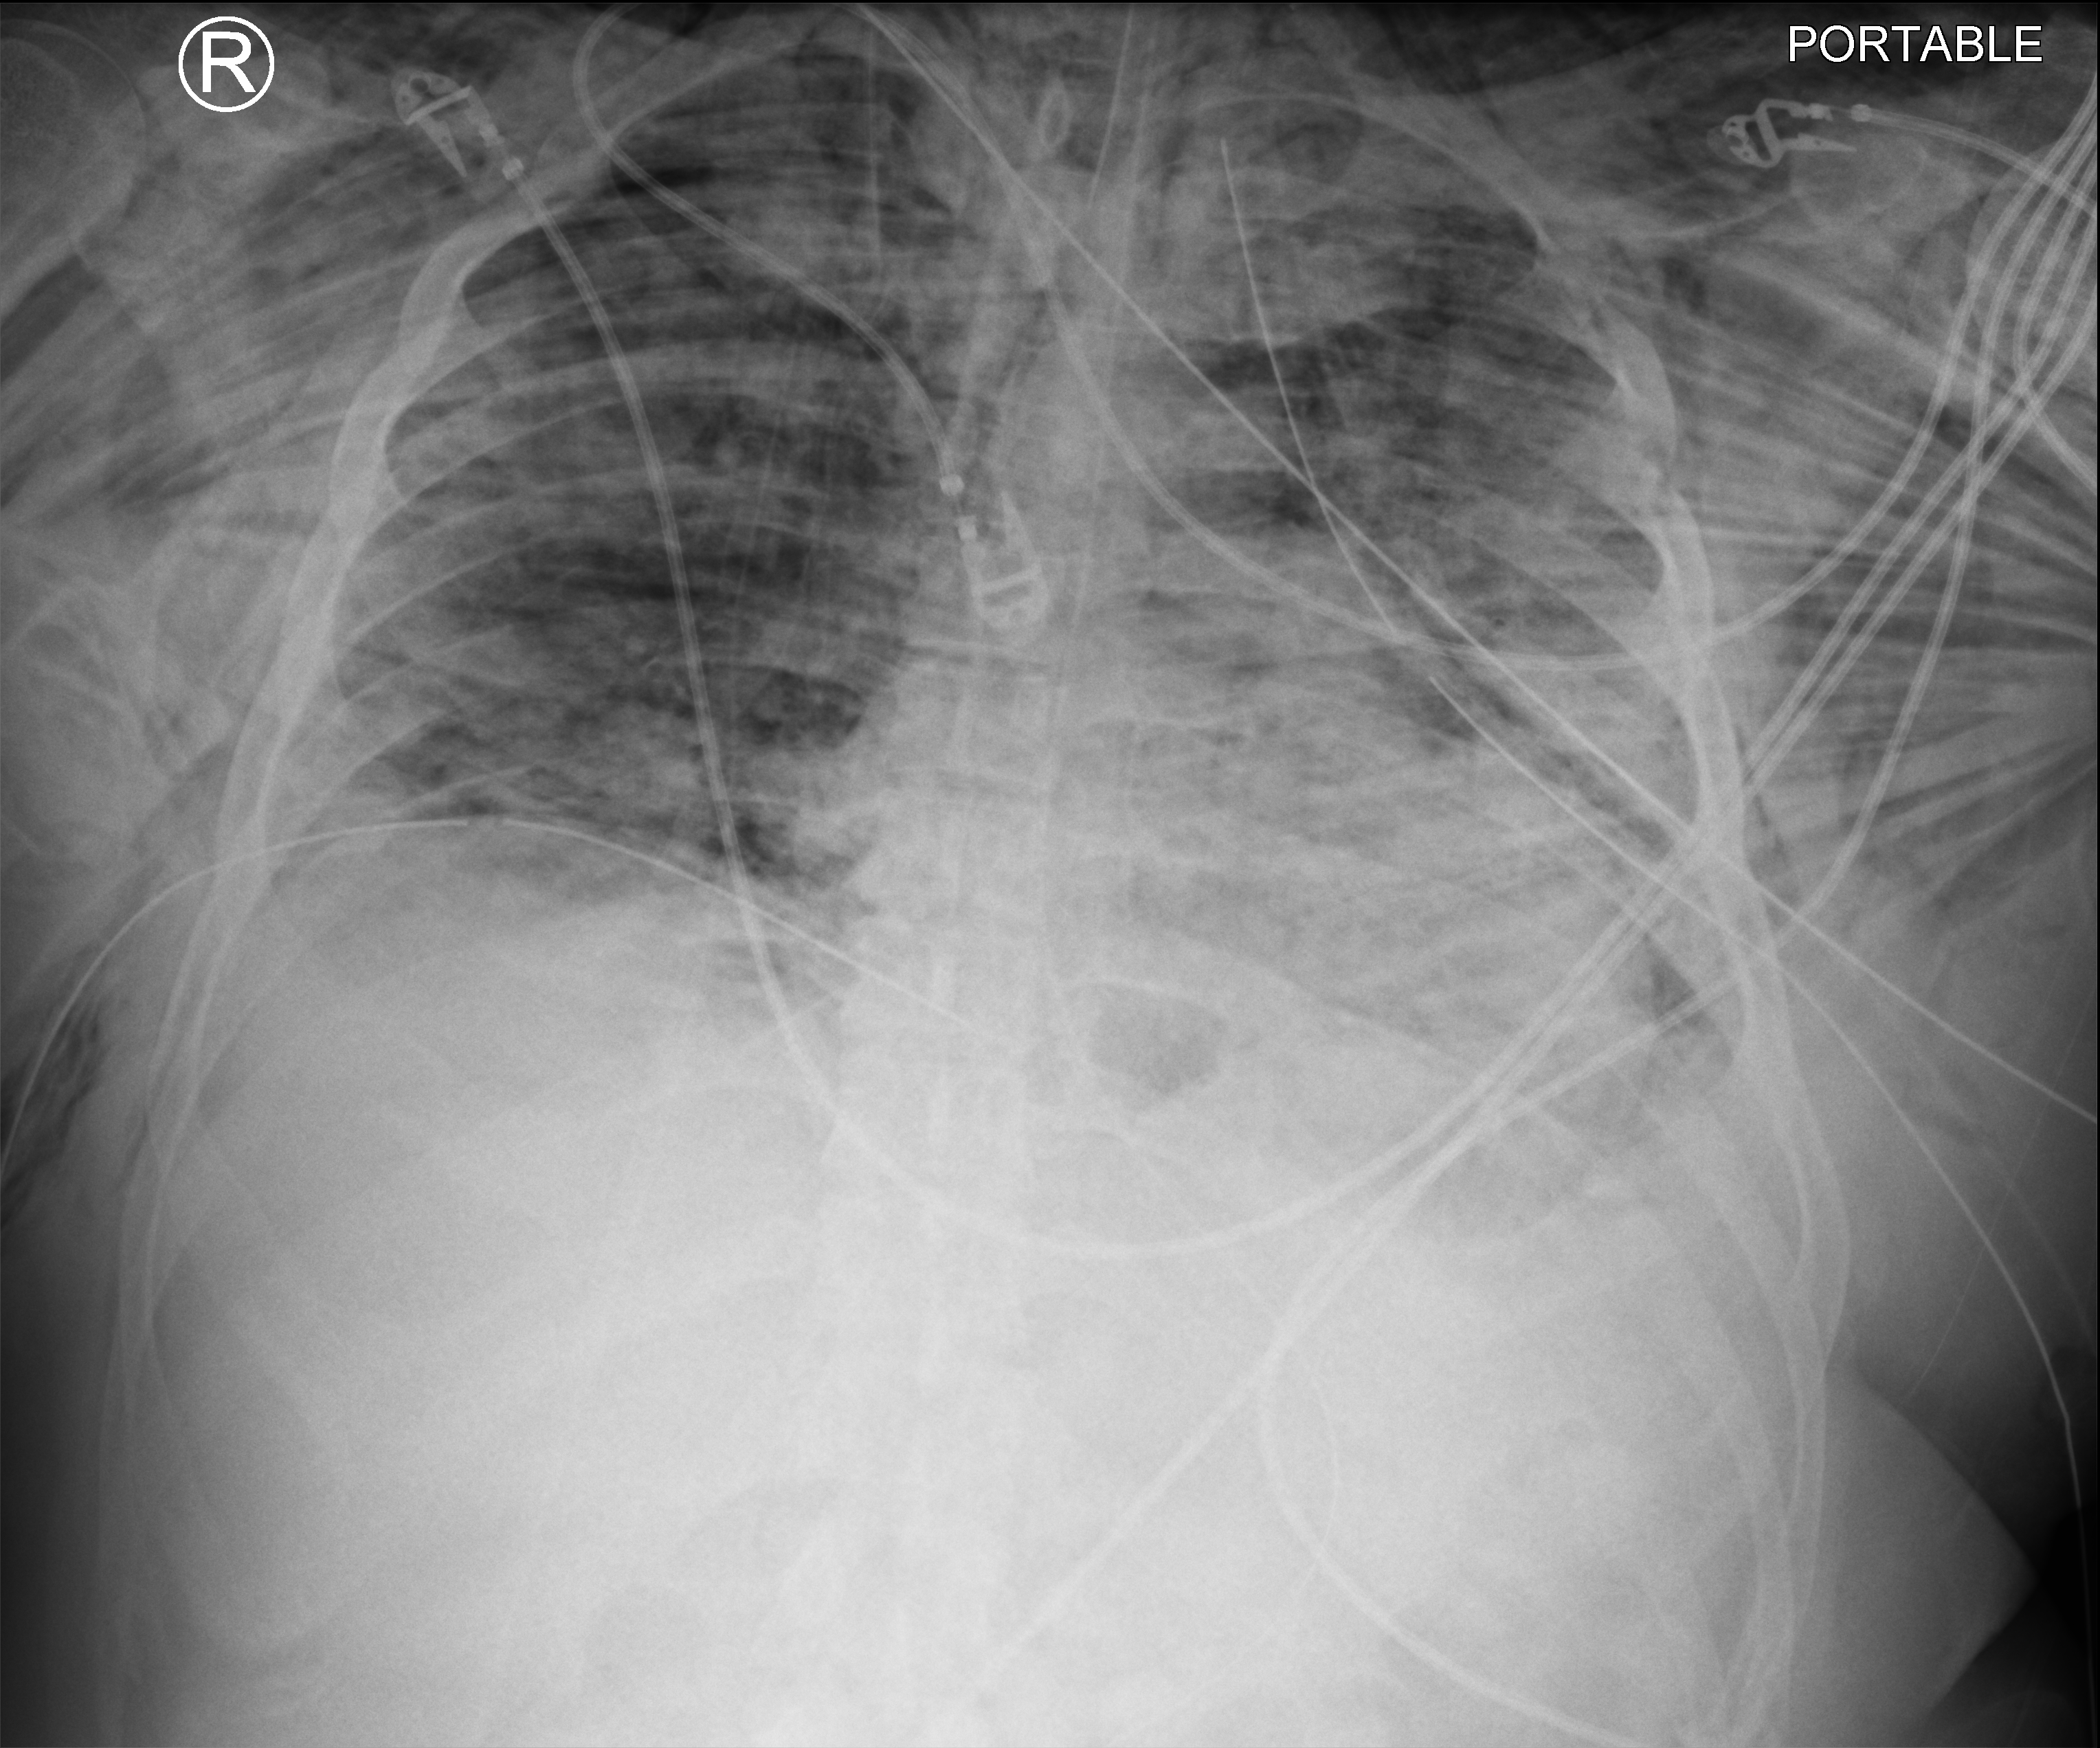
Chest X-ray (portable); anteroposterior (AP) projection. Patient hospitalised with COVID-19; male, aged 18–59 years.
From the hospital-stay record, not from the radiograph (when in the stay this image was taken is not recorded): length of hospital stay: 29 days; admitted to intensive care during this hospital stay: yes; mechanically ventilated during this hospital stay: yes.